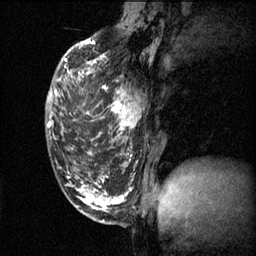
Breast MRI (dynamic contrast-enhanced), one sagittal slice. Position 21 of 60 along the scan axis. 3 images stored at this slice position (order not interpretable as contrast timing). 1.5 T. TE 4.2 ms, TR 11.1 ms. 2 mm slice thickness. 256 × 256 image matrix. Patient: female, 50 years.
Structures marked on this image (semi-automatic segmentation, software-assisted and operator-edited):
- analysis volume of interest (the breast-tissue region the enhancement analysis was run in; not a lesion): bounding box (x1, y1, x2, y2) in pixels: (72, 68, 146, 141)
- tumour enhancement mask (voxels above the 70 % enhancement threshold inside the analysis volume of interest): (72, 68, 141, 141)